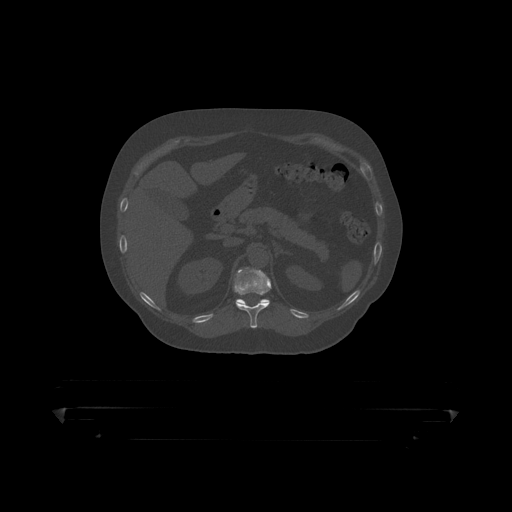
CT including the spine, one axial slice; slice 187 of 390 in the series (ordered by position); reconstruction kernel STANDARD; 120 kVp; bone window (W 1800 / L 400 HU); 512 × 512 image matrix, field of view 650 × 650 mm. Patient: male, 60 years. Case-level facts recorded for this patient, not image findings: primary cancer: prostate.
Annotated regions visible in this slice (semi-automatic segmentation, software-assisted and operator-edited):
- T11 vertebra: bounding box <234,268,272,319> (left, top, right, bottom; pixels)
- T12 vertebra: <236,299,270,304>